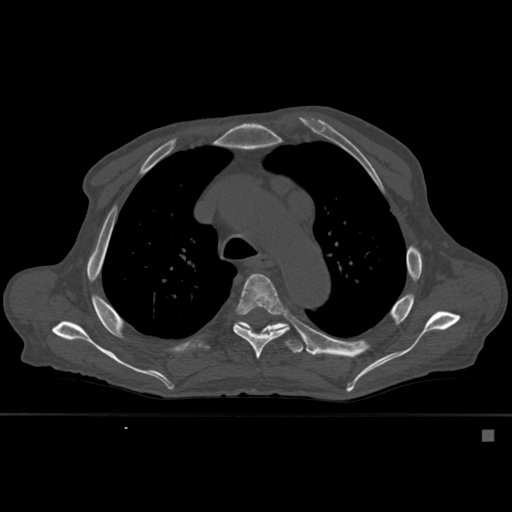
CT including the spine, one axial slice; slice 399 of 527 in the series (ordered by position); bone window (W 1800 / L 400 HU); 1.5 mm slice thickness; 512 × 512 image matrix, field of view 373 × 373 mm. Male patient, age 78 years. Case-level facts recorded for this patient, not image findings: primary cancer: prostate.
Outlined on this slice (semi-automatic segmentation, software-assisted and operator-edited):
- T5 vertebra: box from (x=233, y=273) to (x=290, y=359) px
- T6 vertebra: (x=238, y=323)–(x=304, y=353)